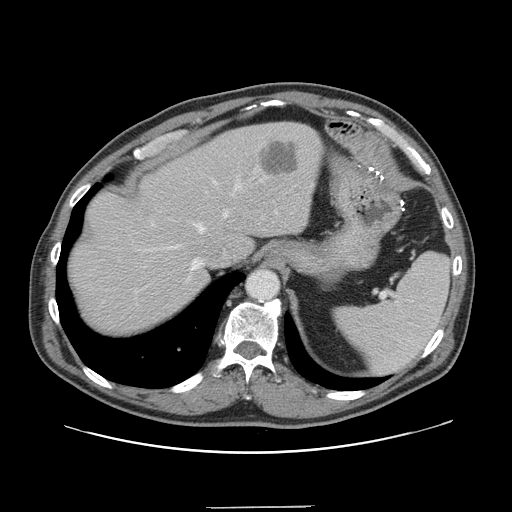
Contrast-enhanced abdominal CT, one axial slice; position 116 of 139 along the scan axis; 120 kVp; intravenous contrast given; soft-tissue window (W 400 / L 40 HU); 512 × 512 image matrix, field of view 397 × 397 mm. Male patient, age 64 years. From the clinical record (not read from this slice): diagnosis: colorectal cancer liver metastases, imaged before liver resection; multiple liver metastases: yes; largest metastasis: 3.5 cm; disease in both lobes: yes.
Outlined on this slice (manually delineated by an expert):
- hepatic veins: box from (x=169, y=181) to (x=237, y=281) px
- liver: (x=68, y=123)–(x=323, y=336)
- planned liver remnant (the part of the liver to remain after resection): (x=68, y=127)–(x=266, y=336)
- liver metastasis: (x=262, y=140)–(x=299, y=176)